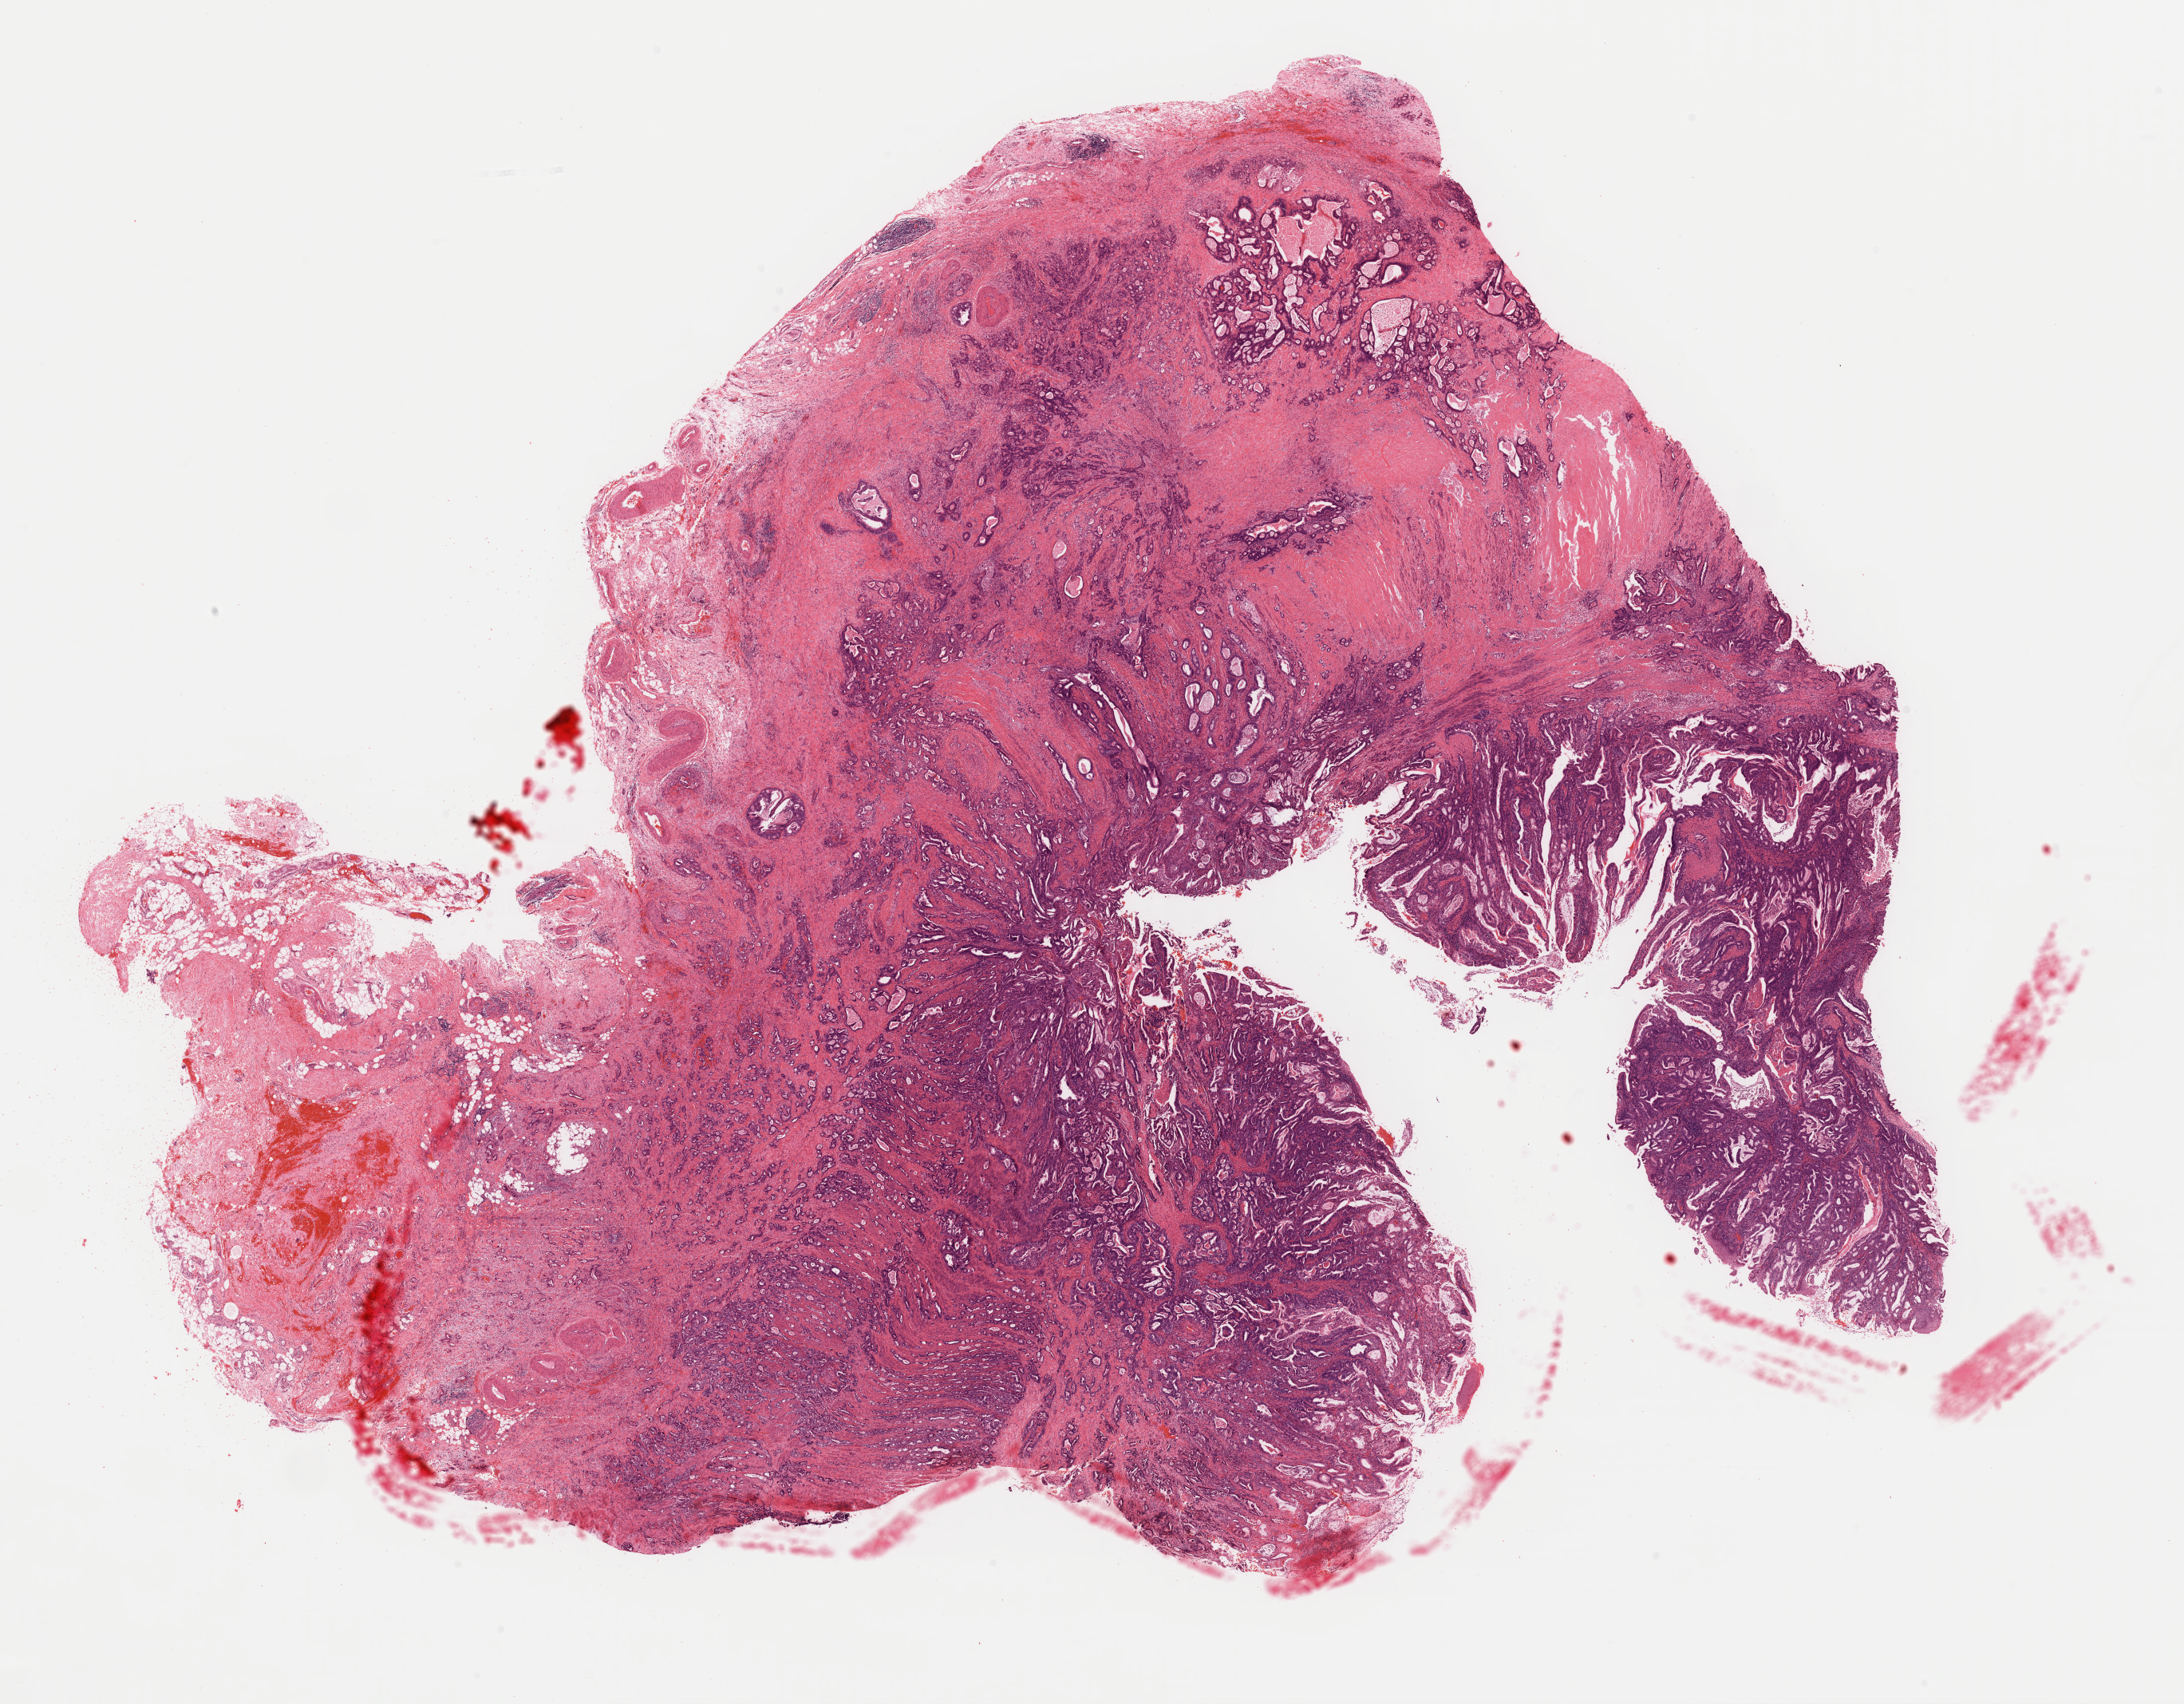
Hematoxylin and eosin (H&E) stained whole-slide image — low-resolution overview of the scanned area, about 21.6 x 16.9 mm (acquisition: 40x scan), formalin-fixed paraffin-embedded (FFPE) diagnostic section, sample: primary tumour, stomach. Male, age 58 years at initial diagnosis. Histologic grade: G3 (poorly differentiated).
TNM: T4a N1 M0. Histologic diagnosis: Adenocarcinoma, NOS (cardia, NOS). AJCC pathologic stage: IIIA. Lymph nodes positive (case pathology): 2 of 3 examined.